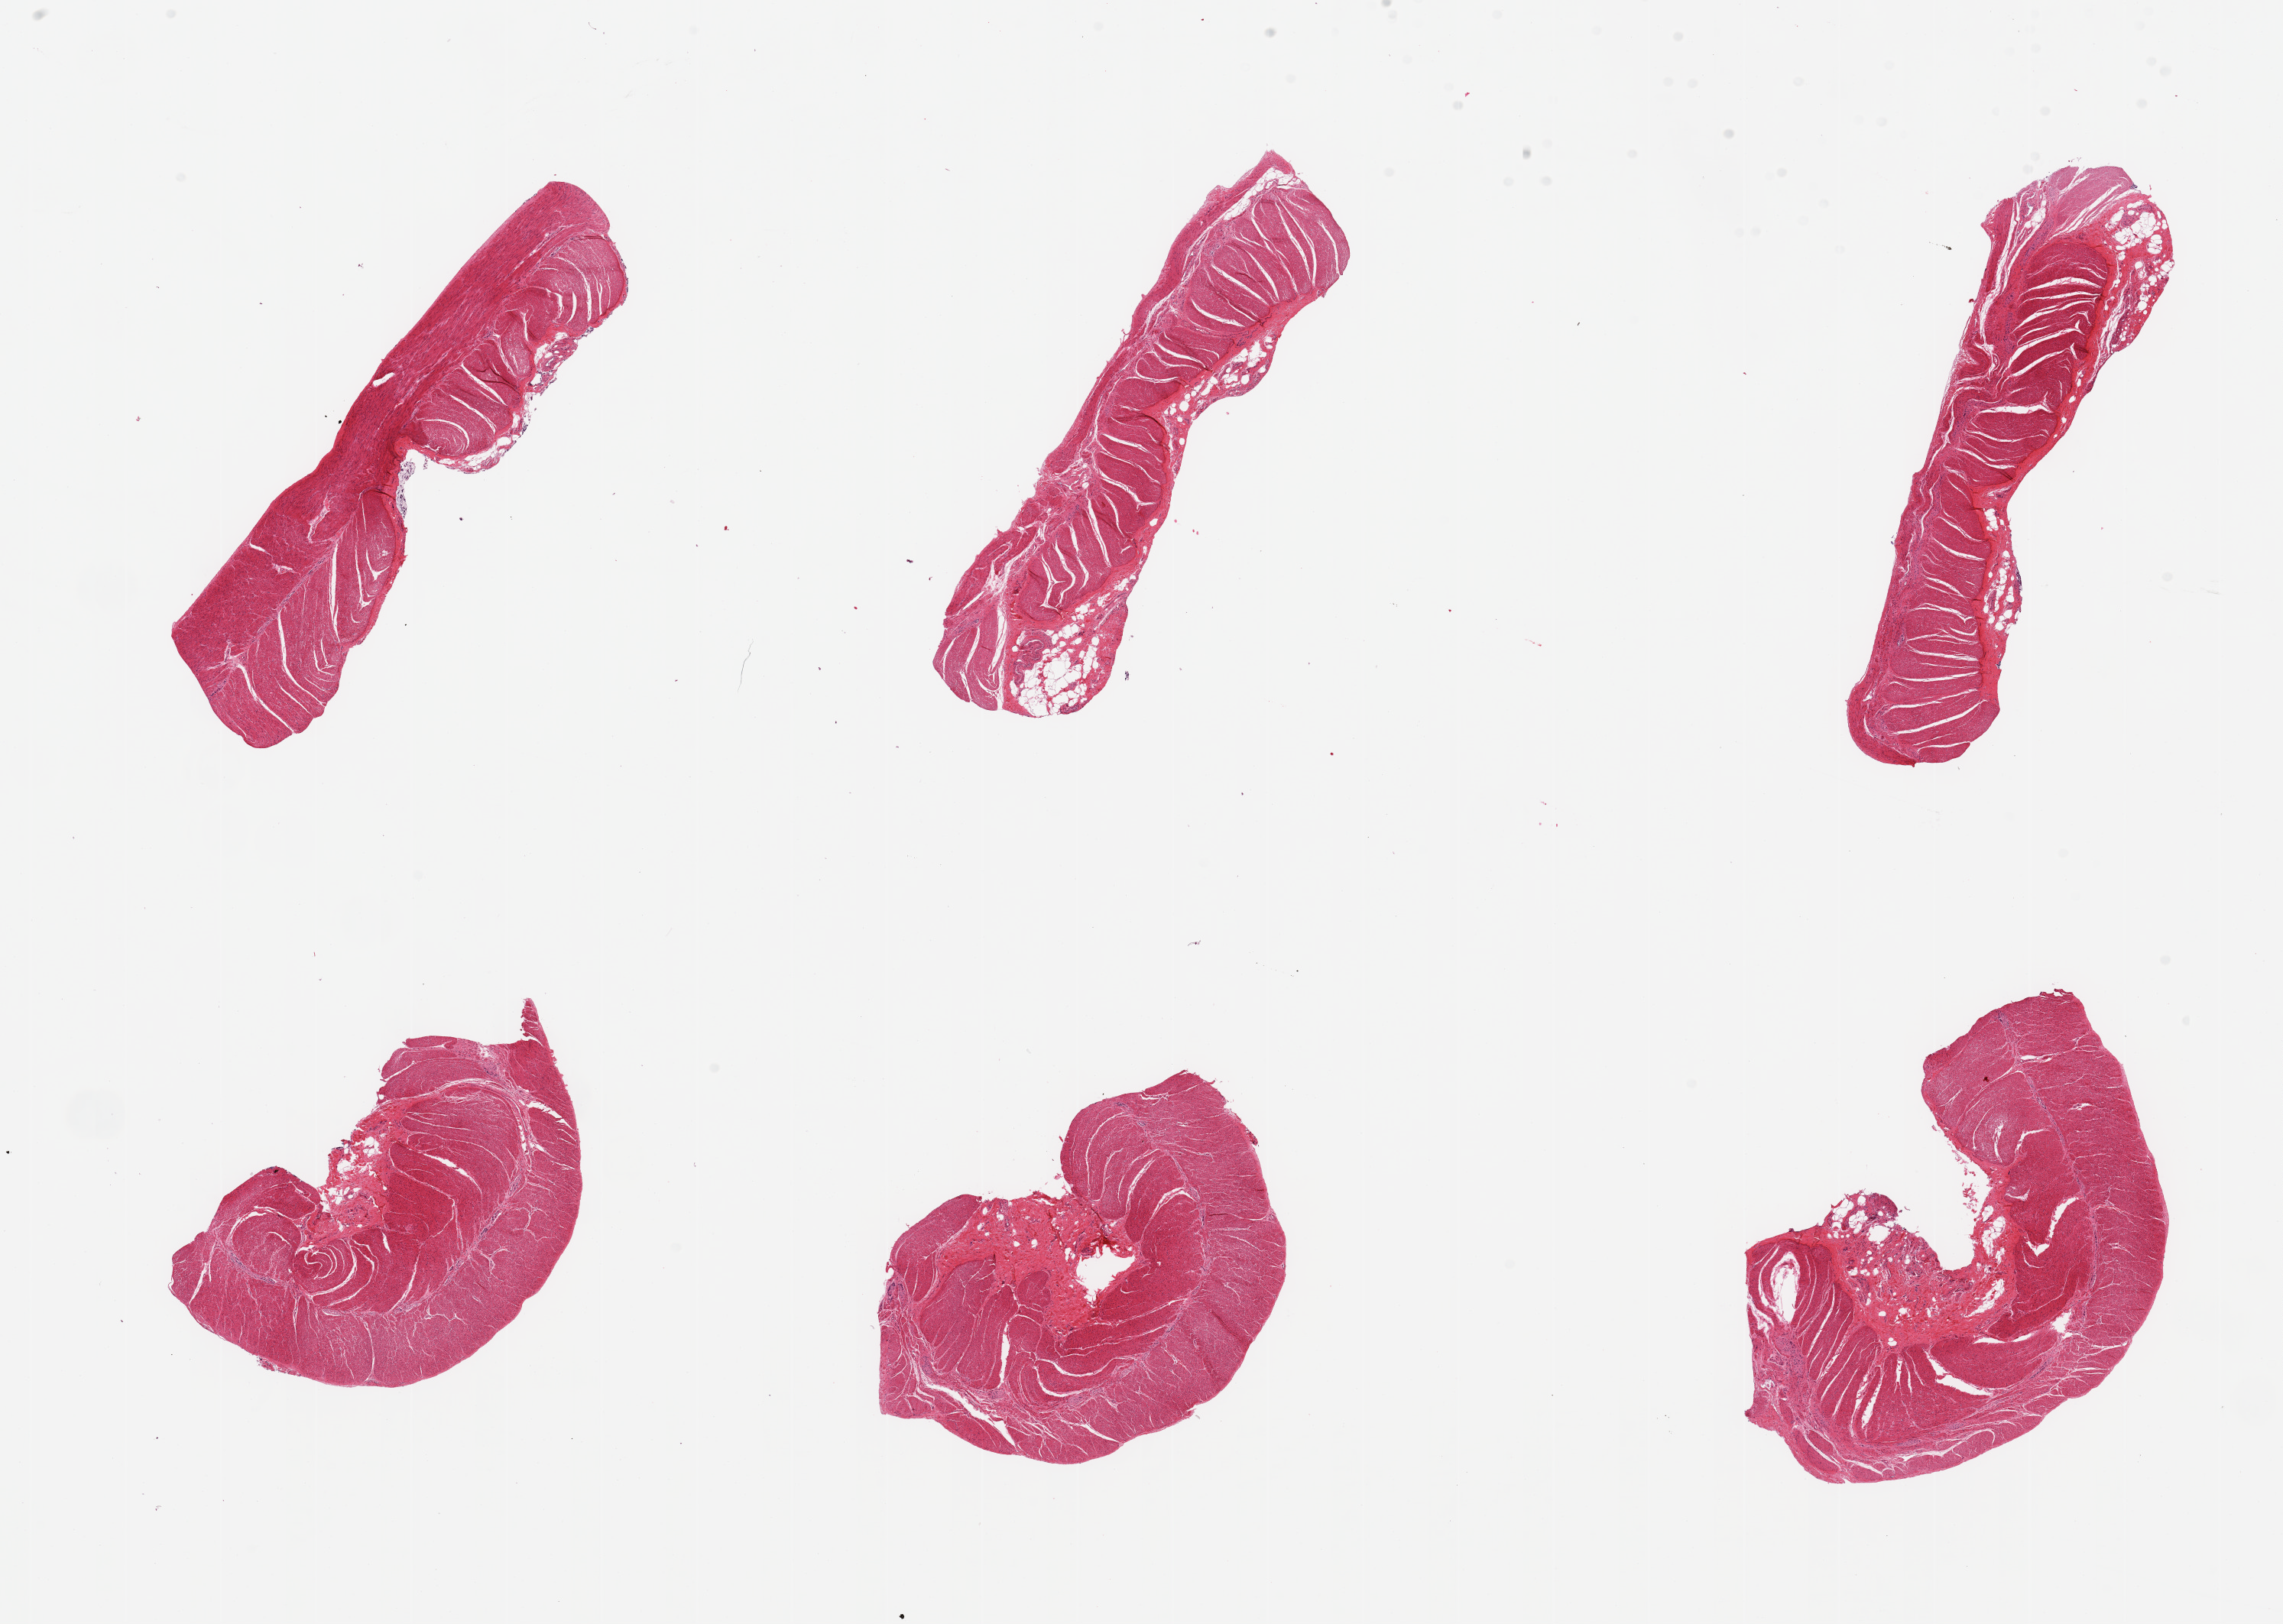
Whole-slide image, hematoxylin and eosin (H&E) stain, brightfield, shown as a low-resolution overview of the whole scanned area (about 23.6 x 16.8 mm), PAXgene-fixed, paraffin-embedded tissue, section of sigmoid colon (target tissue), tissue donor sample. Donor sex: male.
- review note (as recorded): 6 pieces, confirmed target mucsuclaris